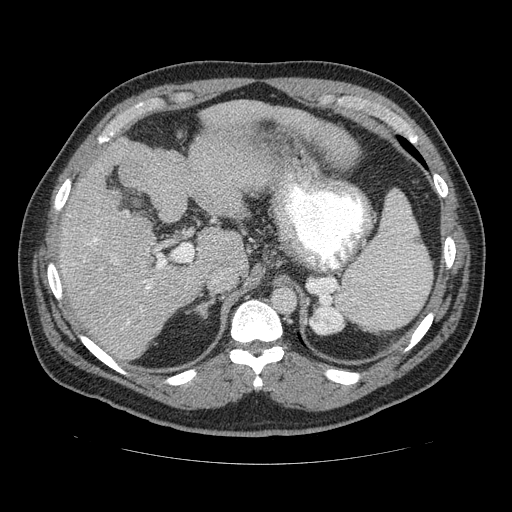
Contrast-enhanced abdominal CT (liver protocol), one axial slice. Slice 86 of 113 in the series (ordered by position). Reconstruction kernel STANDARD. 120 kVp. Soft-tissue window (W 400 / L 40 HU). 512 × 512 image matrix, field of view 400 × 400 mm. Case-level facts recorded for this patient, not image findings: diagnosis: hepatocellular carcinoma (patient treated with transarterial chemoembolisation; whether this scan precedes or follows treatment is not stated here); TNM stage (as recorded): Stage-II; Child-Pugh class: B; tumour differentiation: moderately differentiated; tumour nodularity: multinodular.
Annotated regions visible in this slice (semi-automatically segmented with operator editing):
- liver parenchyma outside the tumour (the mass and vessels are separate outlines, so this box may not span the whole liver): box from (x=50, y=100) to (x=364, y=360) px
- liver vessels: (x=91, y=174)–(x=201, y=295)